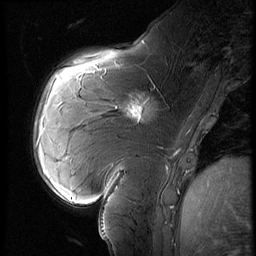
Breast MRI (dynamic contrast-enhanced), one sagittal slice; slice 22 of 60 in the series (ordered by position); 3 images stored at this slice position (order not interpretable as contrast timing); 1.5 T; TE 4.2 ms, TR 9 ms; 2.5 mm slice thickness; 256 × 256 image matrix. Female patient, age 57 years. From the clinical record (not read from this slice): setting: breast cancer imaged before/during neoadjuvant chemotherapy; receptor status: triple-negative.
Structures marked on this image (semi-automatically segmented with operator editing):
- analysis volume of interest (the breast-tissue region the enhancement analysis was run in; not a lesion): box from (x=114, y=83) to (x=170, y=131) px
- tumour enhancement mask (voxels above the 140 % enhancement threshold inside the analysis volume of interest): (x=128, y=104)–(x=143, y=120)